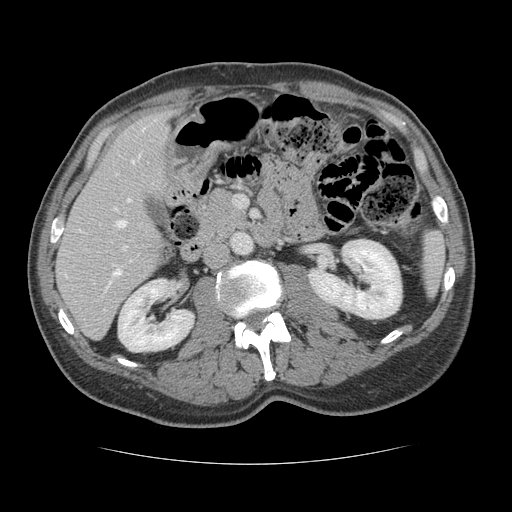
Contrast-enhanced abdominal CT, one axial slice; position 59 of 134 along the scan axis; reconstruction kernel STANDARD; intravenous contrast given; soft-tissue window (W 400 / L 40 HU); 2.5 mm slice thickness; 512 × 512 image matrix, field of view 377 × 377 mm. Male patient, age 68 years. Case-level facts recorded for this patient, not image findings: diagnosis: colorectal cancer liver metastases, imaged before liver resection; multiple liver metastases: yes; largest metastasis: 2.2 cm; disease in both lobes: no.
Outlined on this slice (outlined manually by an expert reader):
- hepatic veins: bounding box [x1, y1, x2, y2] px = [116, 129, 144, 228]
- liver: [58, 112, 171, 338]
- planned liver remnant (the part of the liver to remain after resection): [57, 112, 172, 335]
- portal vein (with intrahepatic branches): [107, 208, 127, 287]